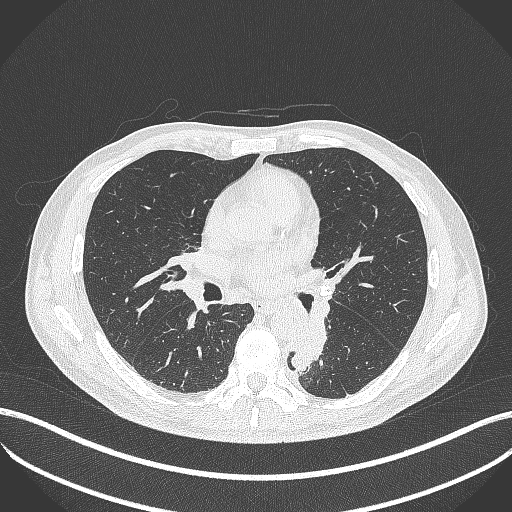
Chest CT, one axial slice; slice 217 of 451 in the series (ordered by position); 120 kVp; lung window (W 1500 / L -600 HU); 512 × 512 image matrix, field of view 400 × 400 mm. Patient: male, 72 years. Case-level facts recorded for this patient, not image findings: clinical TNM (as recorded): T2b N0 M1.
Annotated regions visible in this slice (rectangle marked by the reading radiologist):
- lung tumour (recorded histology: adenocarcinoma): box from (x=285, y=316) to (x=335, y=375) px